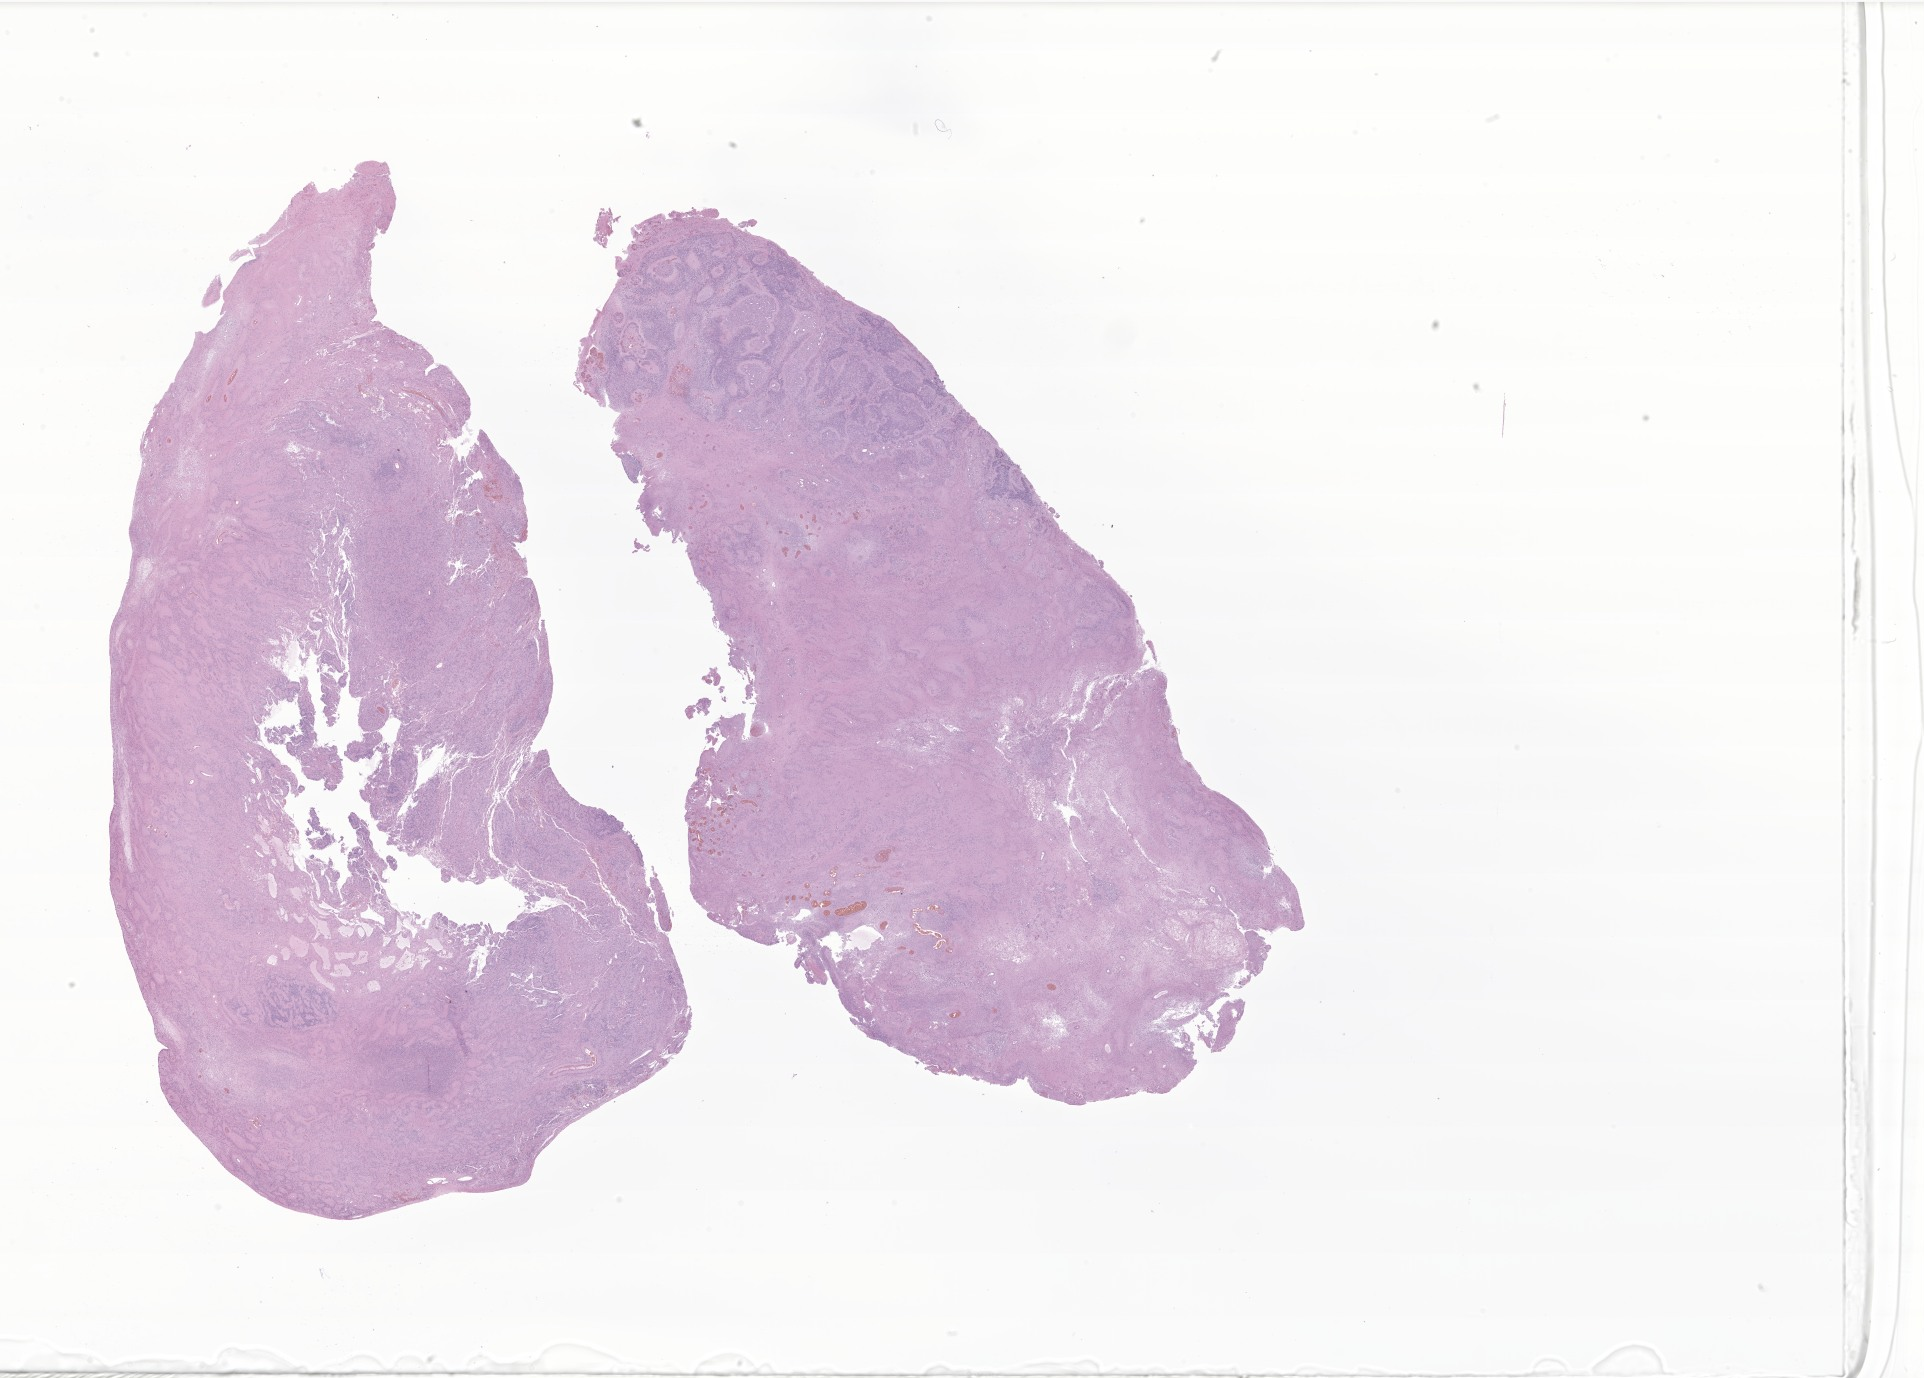
Digitized haematoxylin and eosin-stained section of tumor tissue from the cerebellum — low-resolution overview of the scanned area, about 32.4 x 23.2 mm, formalin-fixed, paraffin-embedded (FFPE) tissue. Patient female; age 761 days (about 2.1 years).
- recorded diagnosis: Ependymoma, NOS